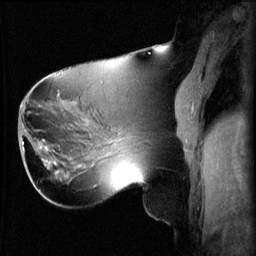
Breast MRI (dynamic contrast-enhanced), one sagittal slice; slice 28 of 60 in the series (ordered by position); 3 images stored at this slice position (order not interpretable as contrast timing); 1.5 T; TE 4.2 ms, TR 8.2 ms; 2.2 mm slice thickness; 256 × 256 image matrix, field of view 220 × 220 mm. Female patient, age 62 years.
Structures marked on this image (semi-automatically segmented with operator editing):
- analysis volume of interest (the breast-tissue region the enhancement analysis was run in; not a lesion): bounding box <26,130,59,165> (left, top, right, bottom; pixels)
- tumour enhancement mask (voxels above the 70 % enhancement threshold inside the analysis volume of interest): <46,146,57,165>